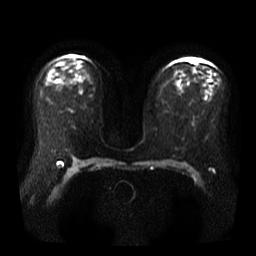
Breast MRI, one axial slice. Position 24 of 40 along the scan axis. Diffusion-weighted series; image 2 of 4 stored at this slice position (different b-values; order by instance number). 3 T. 5 mm slice thickness. 256 × 256 image matrix, field of view 360 × 360 mm. Female patient.
Annotated regions visible in this slice (outlined manually by an expert reader):
- tumour on diffusion-weighted imaging: box from (x=192, y=58) to (x=201, y=65) px